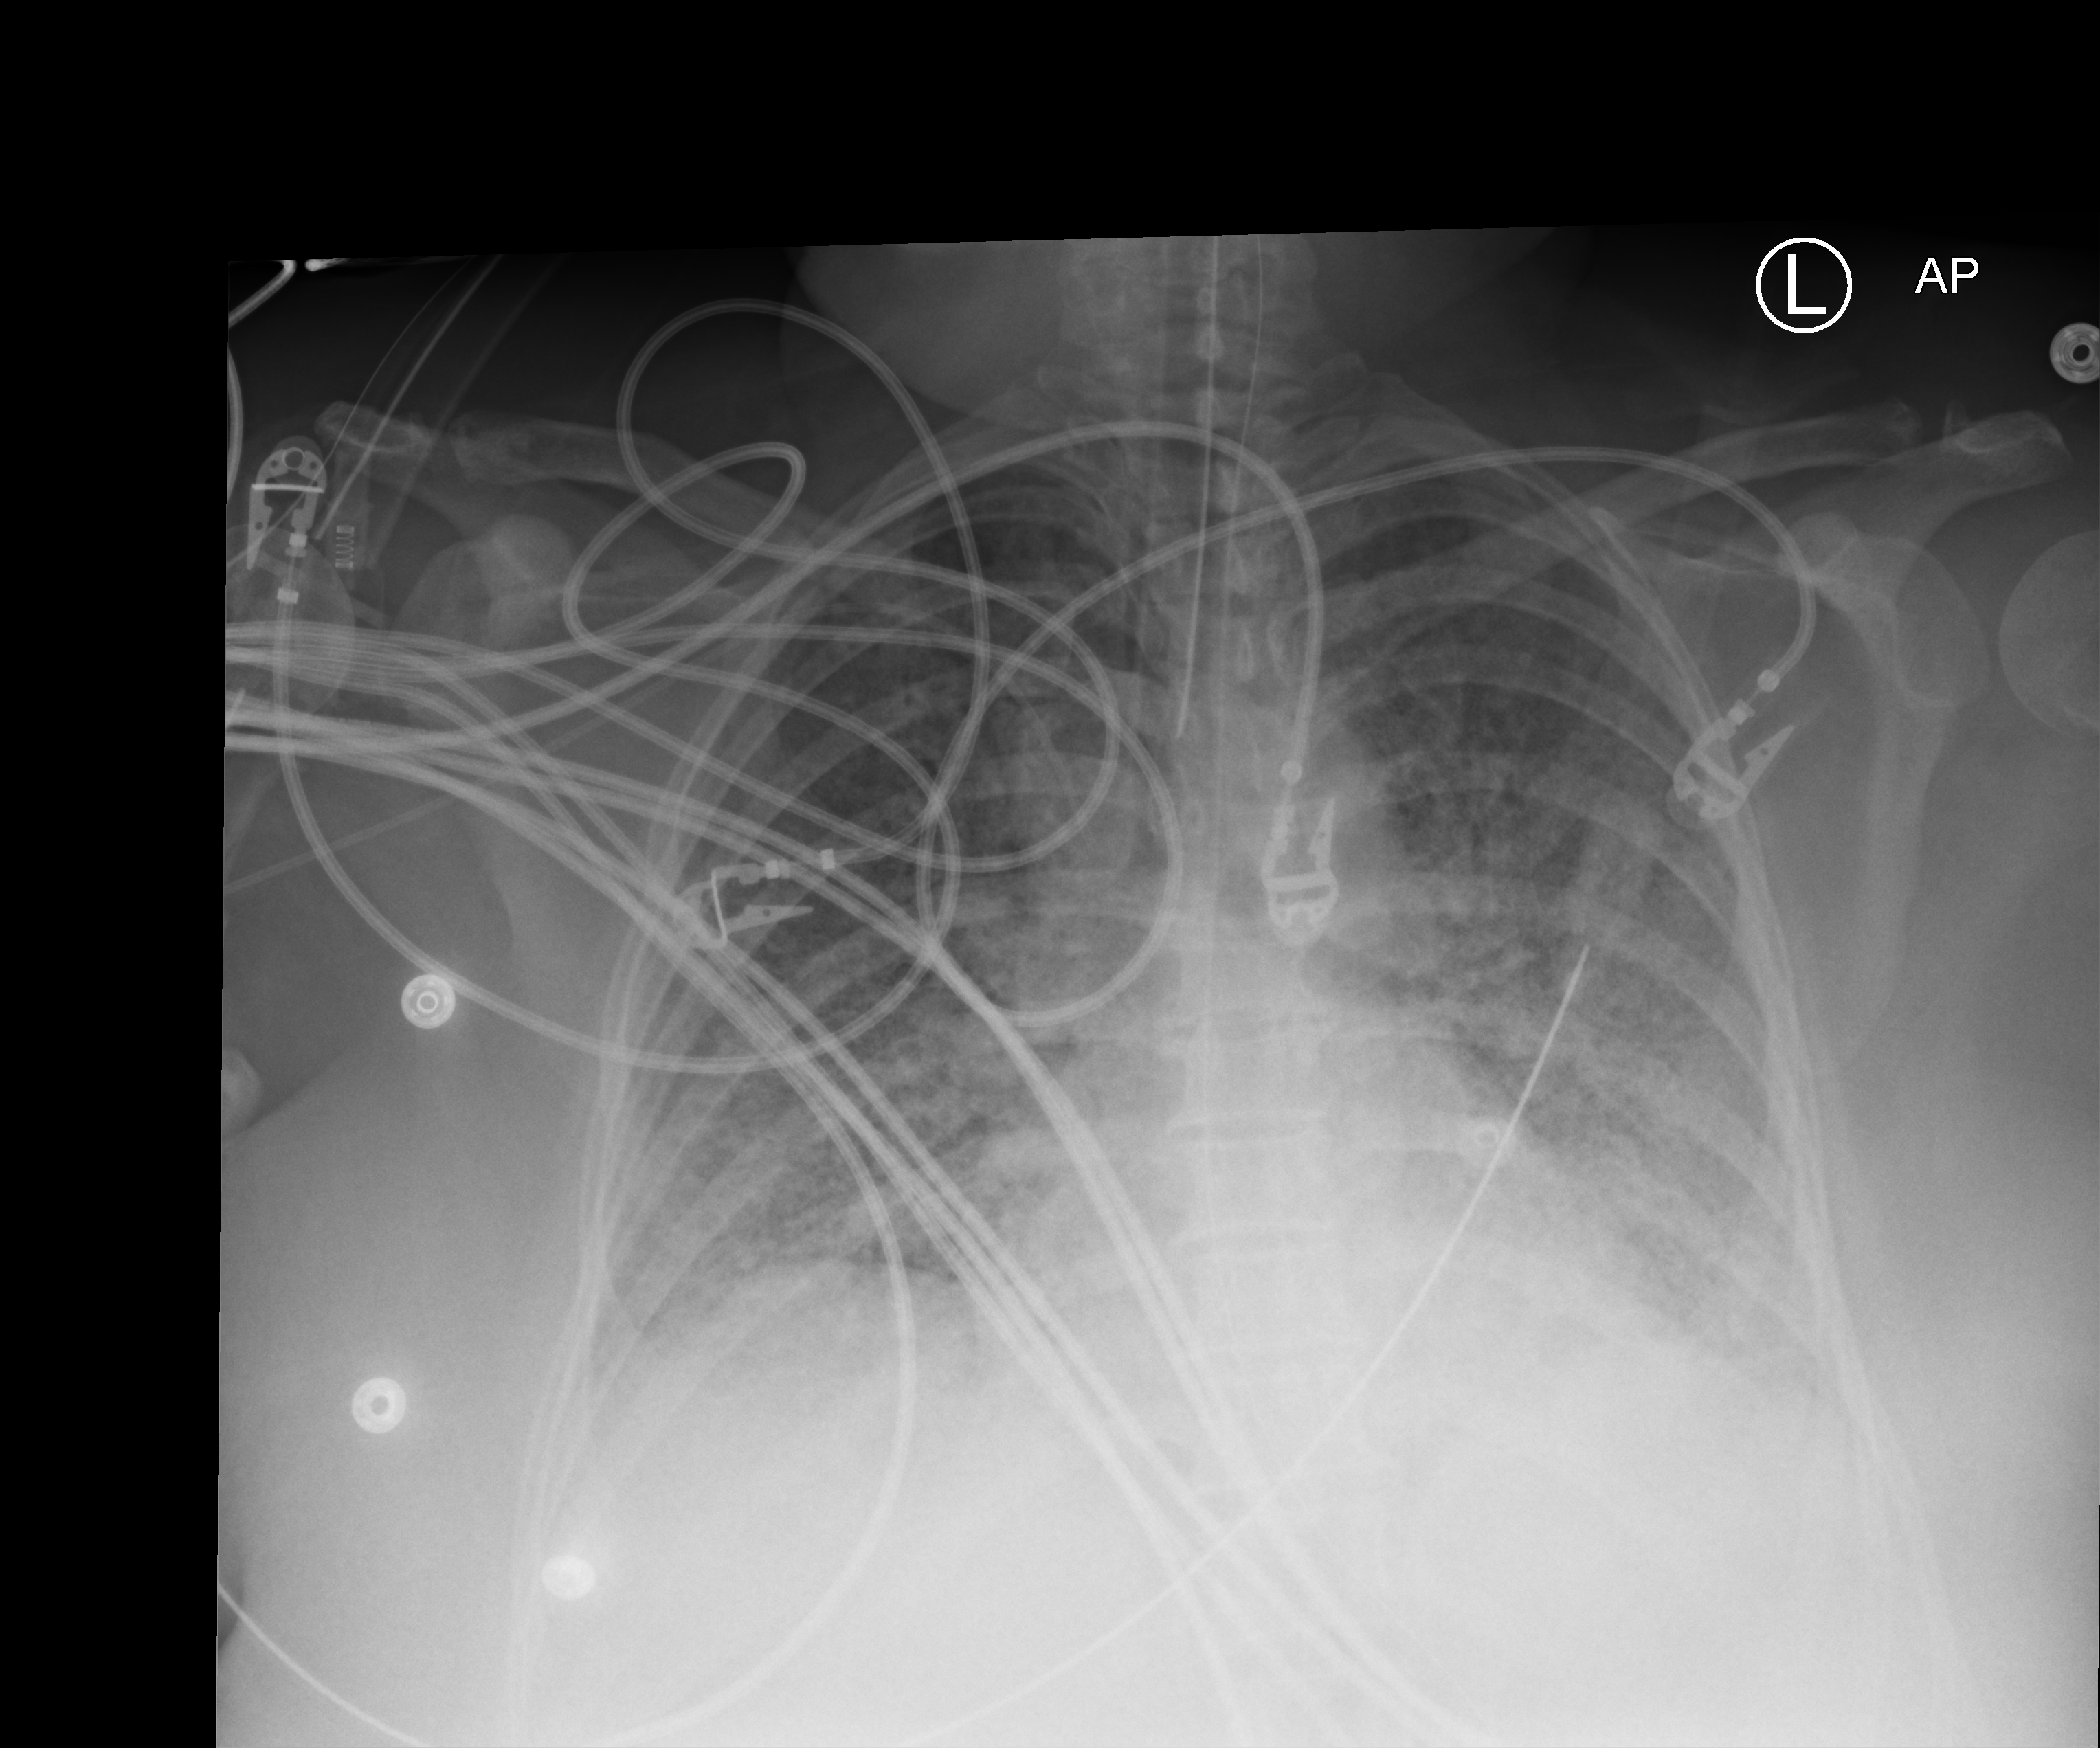
Chest X-ray (portable), anteroposterior (AP) projection. Female patient hospitalised with COVID-19, age 18–59 years.
From the hospital-stay record, not from the radiograph (when in the stay this image was taken is not recorded): mechanically ventilated during this hospital stay: yes; other chronic lung disease (admission record): no.